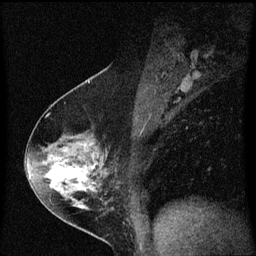
Breast MRI (dynamic contrast-enhanced), one sagittal slice. Position 34 of 60 along the scan axis. Dynamic contrast-enhanced series, image 2 of 3 at this slice position (ordered by acquisition). 1.5 T. TE 4.2 ms, TR 8.4 ms. 2 mm slice thickness. 256 × 256 image matrix, field of view 200 × 200 mm. Female patient, age 54 years. From the clinical record (not read from this slice): setting: breast cancer imaged before/during neoadjuvant chemotherapy; receptor status: HER2-positive.
Outlined on this slice (semi-automatically segmented with operator editing):
- analysis volume of interest (the breast-tissue region the enhancement analysis was run in; not a lesion): bounding box [x1, y1, x2, y2] px = [32, 122, 121, 213]
- tumour enhancement mask (voxels above the 70 % enhancement threshold inside the analysis volume of interest): [48, 166, 95, 191]